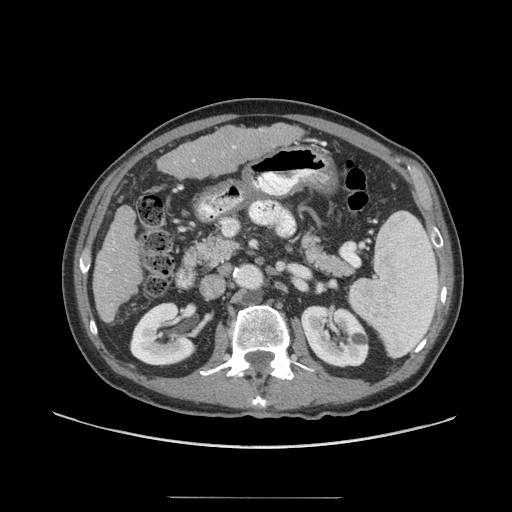
Contrast-enhanced abdominal CT (liver protocol), one axial slice; slice 21 of 71 in the series (ordered by position); soft-tissue window (W 400 / L 40 HU); 2.5 mm slice thickness; 512 × 512 image matrix. Case-level facts recorded for this patient, not image findings: diagnosis: hepatocellular carcinoma (patient treated with transarterial chemoembolisation; whether this scan precedes or follows treatment is not stated here); TNM stage (as recorded): Stage-I; Child-Pugh class: A; tumour differentiation: well differentiated; tumour size: 3.5 cm.
Annotated regions visible in this slice (semi-automatic segmentation, software-assisted and operator-edited):
- liver parenchyma outside the tumour (the mass and vessels are separate outlines, so this box may not span the whole liver): bounding box (x1, y1, x2, y2) in pixels: (92, 122, 302, 322)
- liver vessels: (104, 146, 236, 270)